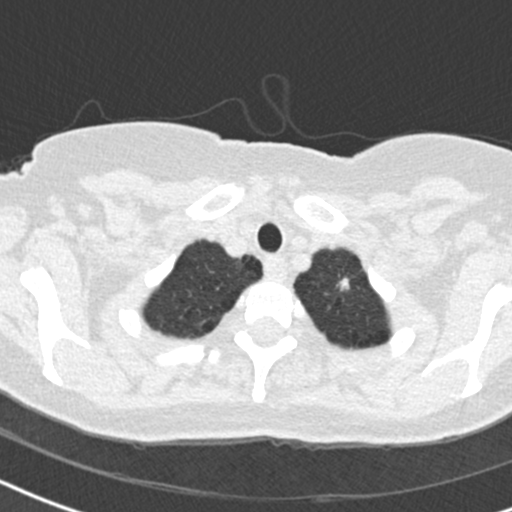
Low-dose screening chest CT, one axial slice; slice 170 of 184 in the series (ordered by position); reconstruction kernel B30f; 120 kVp; lung window (W 1500 / L -600 HU); 2 mm slice thickness; 512 × 512 image matrix, field of view 280 × 280 mm.
Structures marked on this image (manually delineated by an expert):
- lesion 1 (tumor, upper lobe of left lung): bounding box (x1, y1, x2, y2) in pixels: (337, 278, 350, 291)